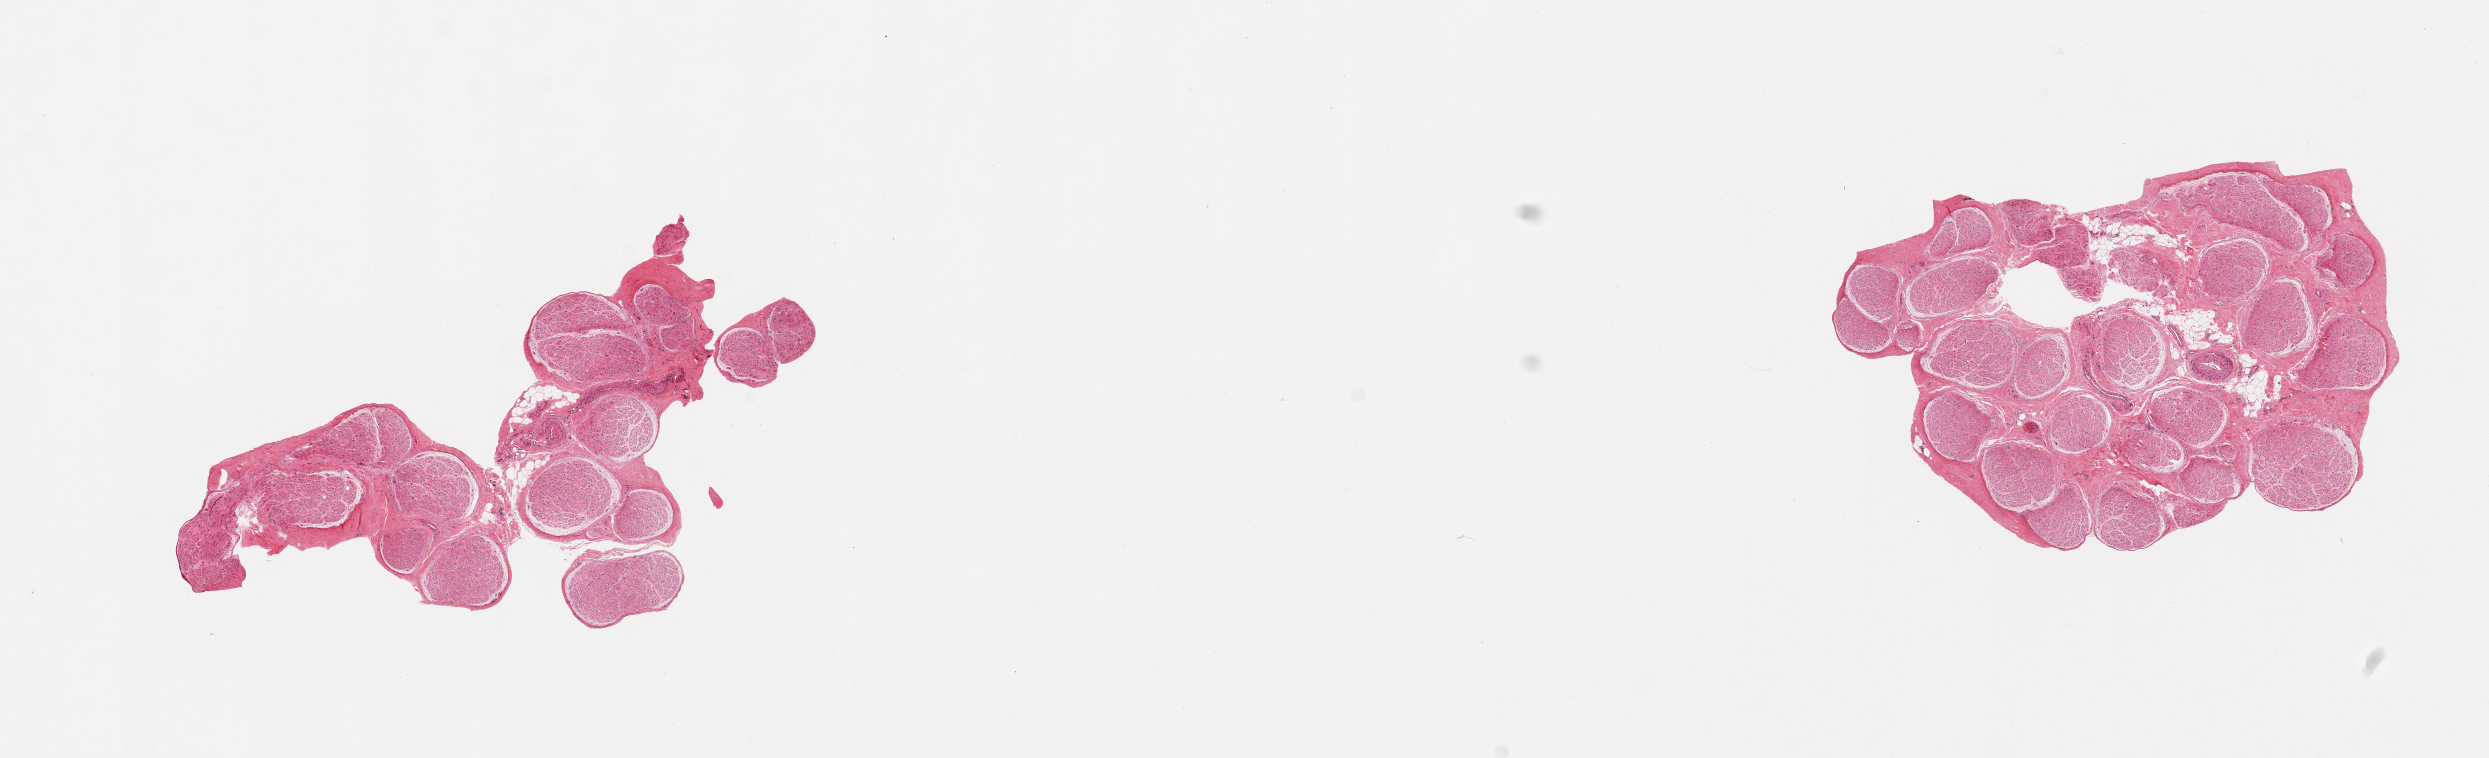
Digitized hematoxylin and eosin (H&E)-stained section, whole scanned area (about 19.7 x 6.0 mm, slide scanned at 20x) shown as a low-resolution overview. PAXgene-fixed paraffin-embedded (PFPE) section. Sampled site (target tissue): tibial nerve. Tissue donor sample. Donor sex: male.
* reviewer comment on this tissue sample: 2 pieces; well trimmed, minimal internal fat